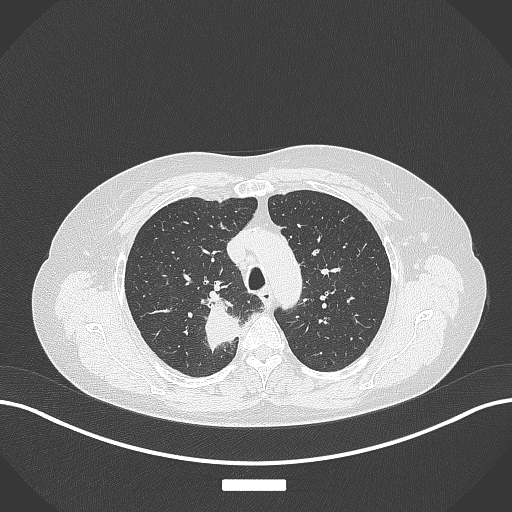
Chest CT, one axial slice; position 289 of 357 along the scan axis; lung window (W 1500 / L -600 HU); 1 mm slice thickness; 512 × 512 image matrix. Female patient, age 62 years. From the clinical record (not read from this slice): clinical TNM (as recorded): T1c N1 M0.
Annotated regions visible in this slice (bounding box drawn by a radiologist):
- lung tumour (recorded histology: squamous cell carcinoma): bounding box (x1, y1, x2, y2) in pixels: (198, 290, 238, 361)